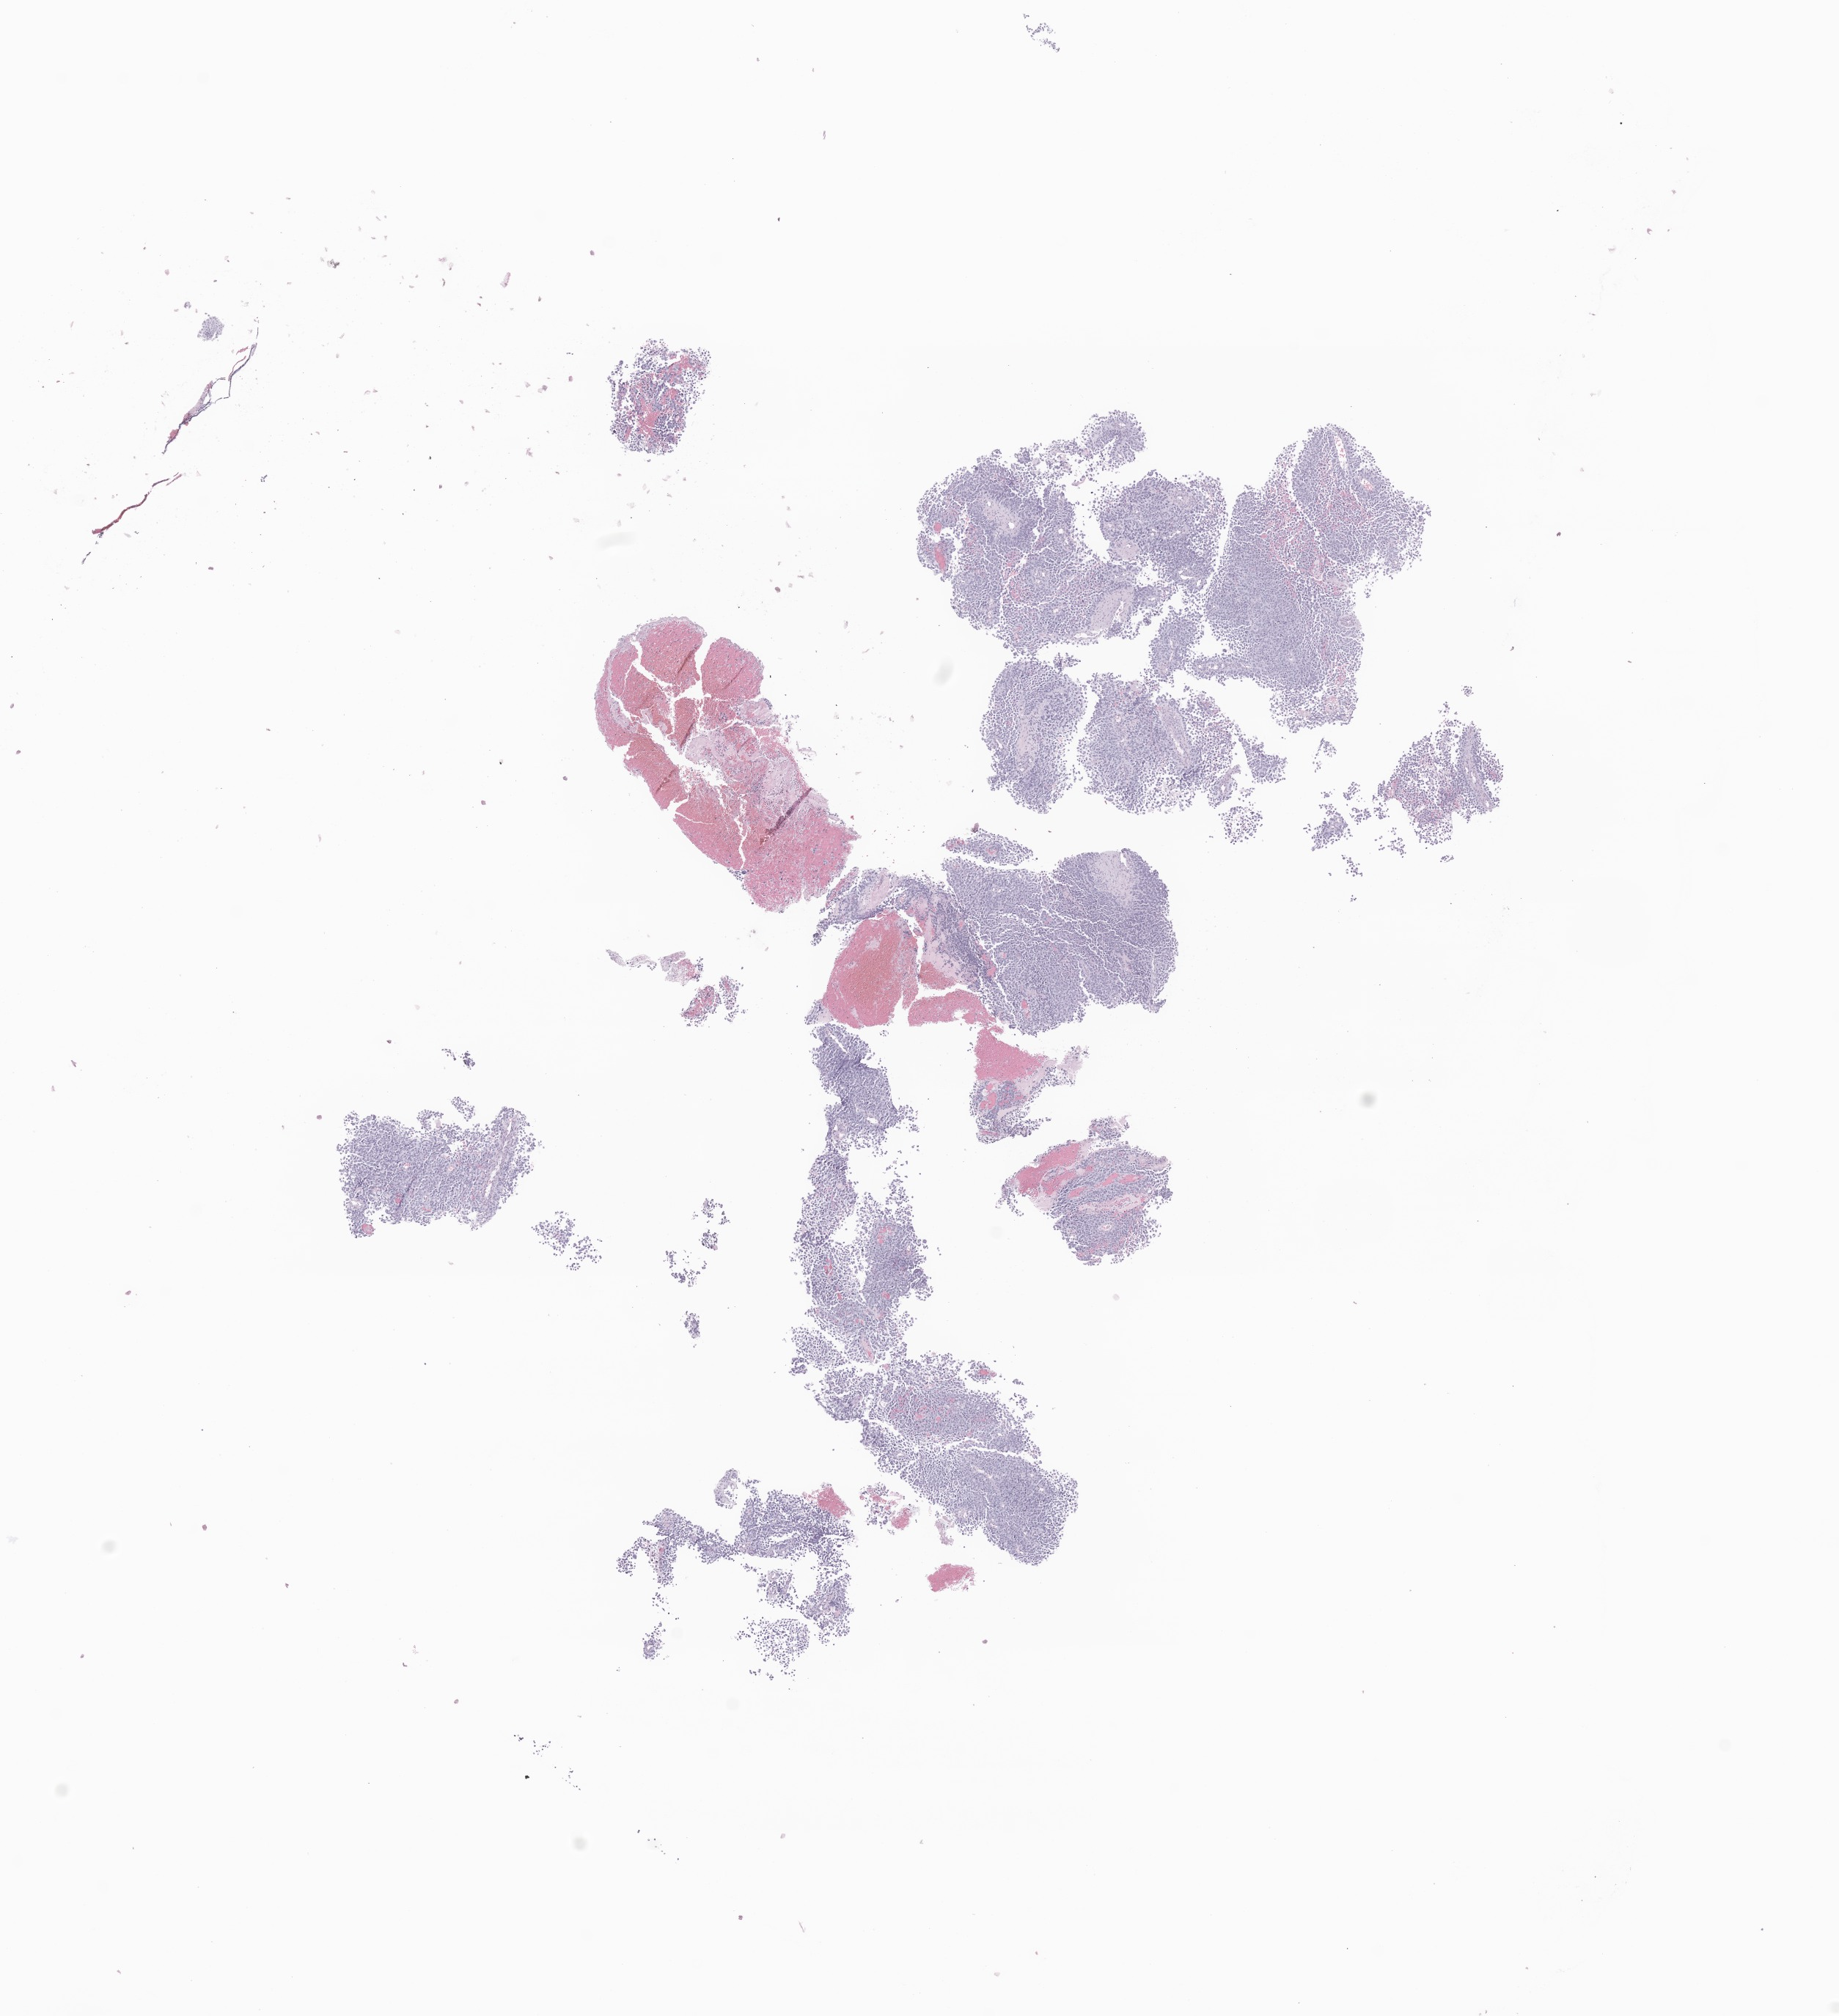
Hematoxylin and eosin (H&E) whole-slide image of tumor tissue from the pelvis, a low-resolution overview of the entire scanned area, about 10.6 x 11.6 mm. Formalin-fixed, paraffin-embedded (FFPE) tissue. Patient female; age 35 months (2 years 11 months).
Diagnosis: Rhabdomyosarcoma, NOS.